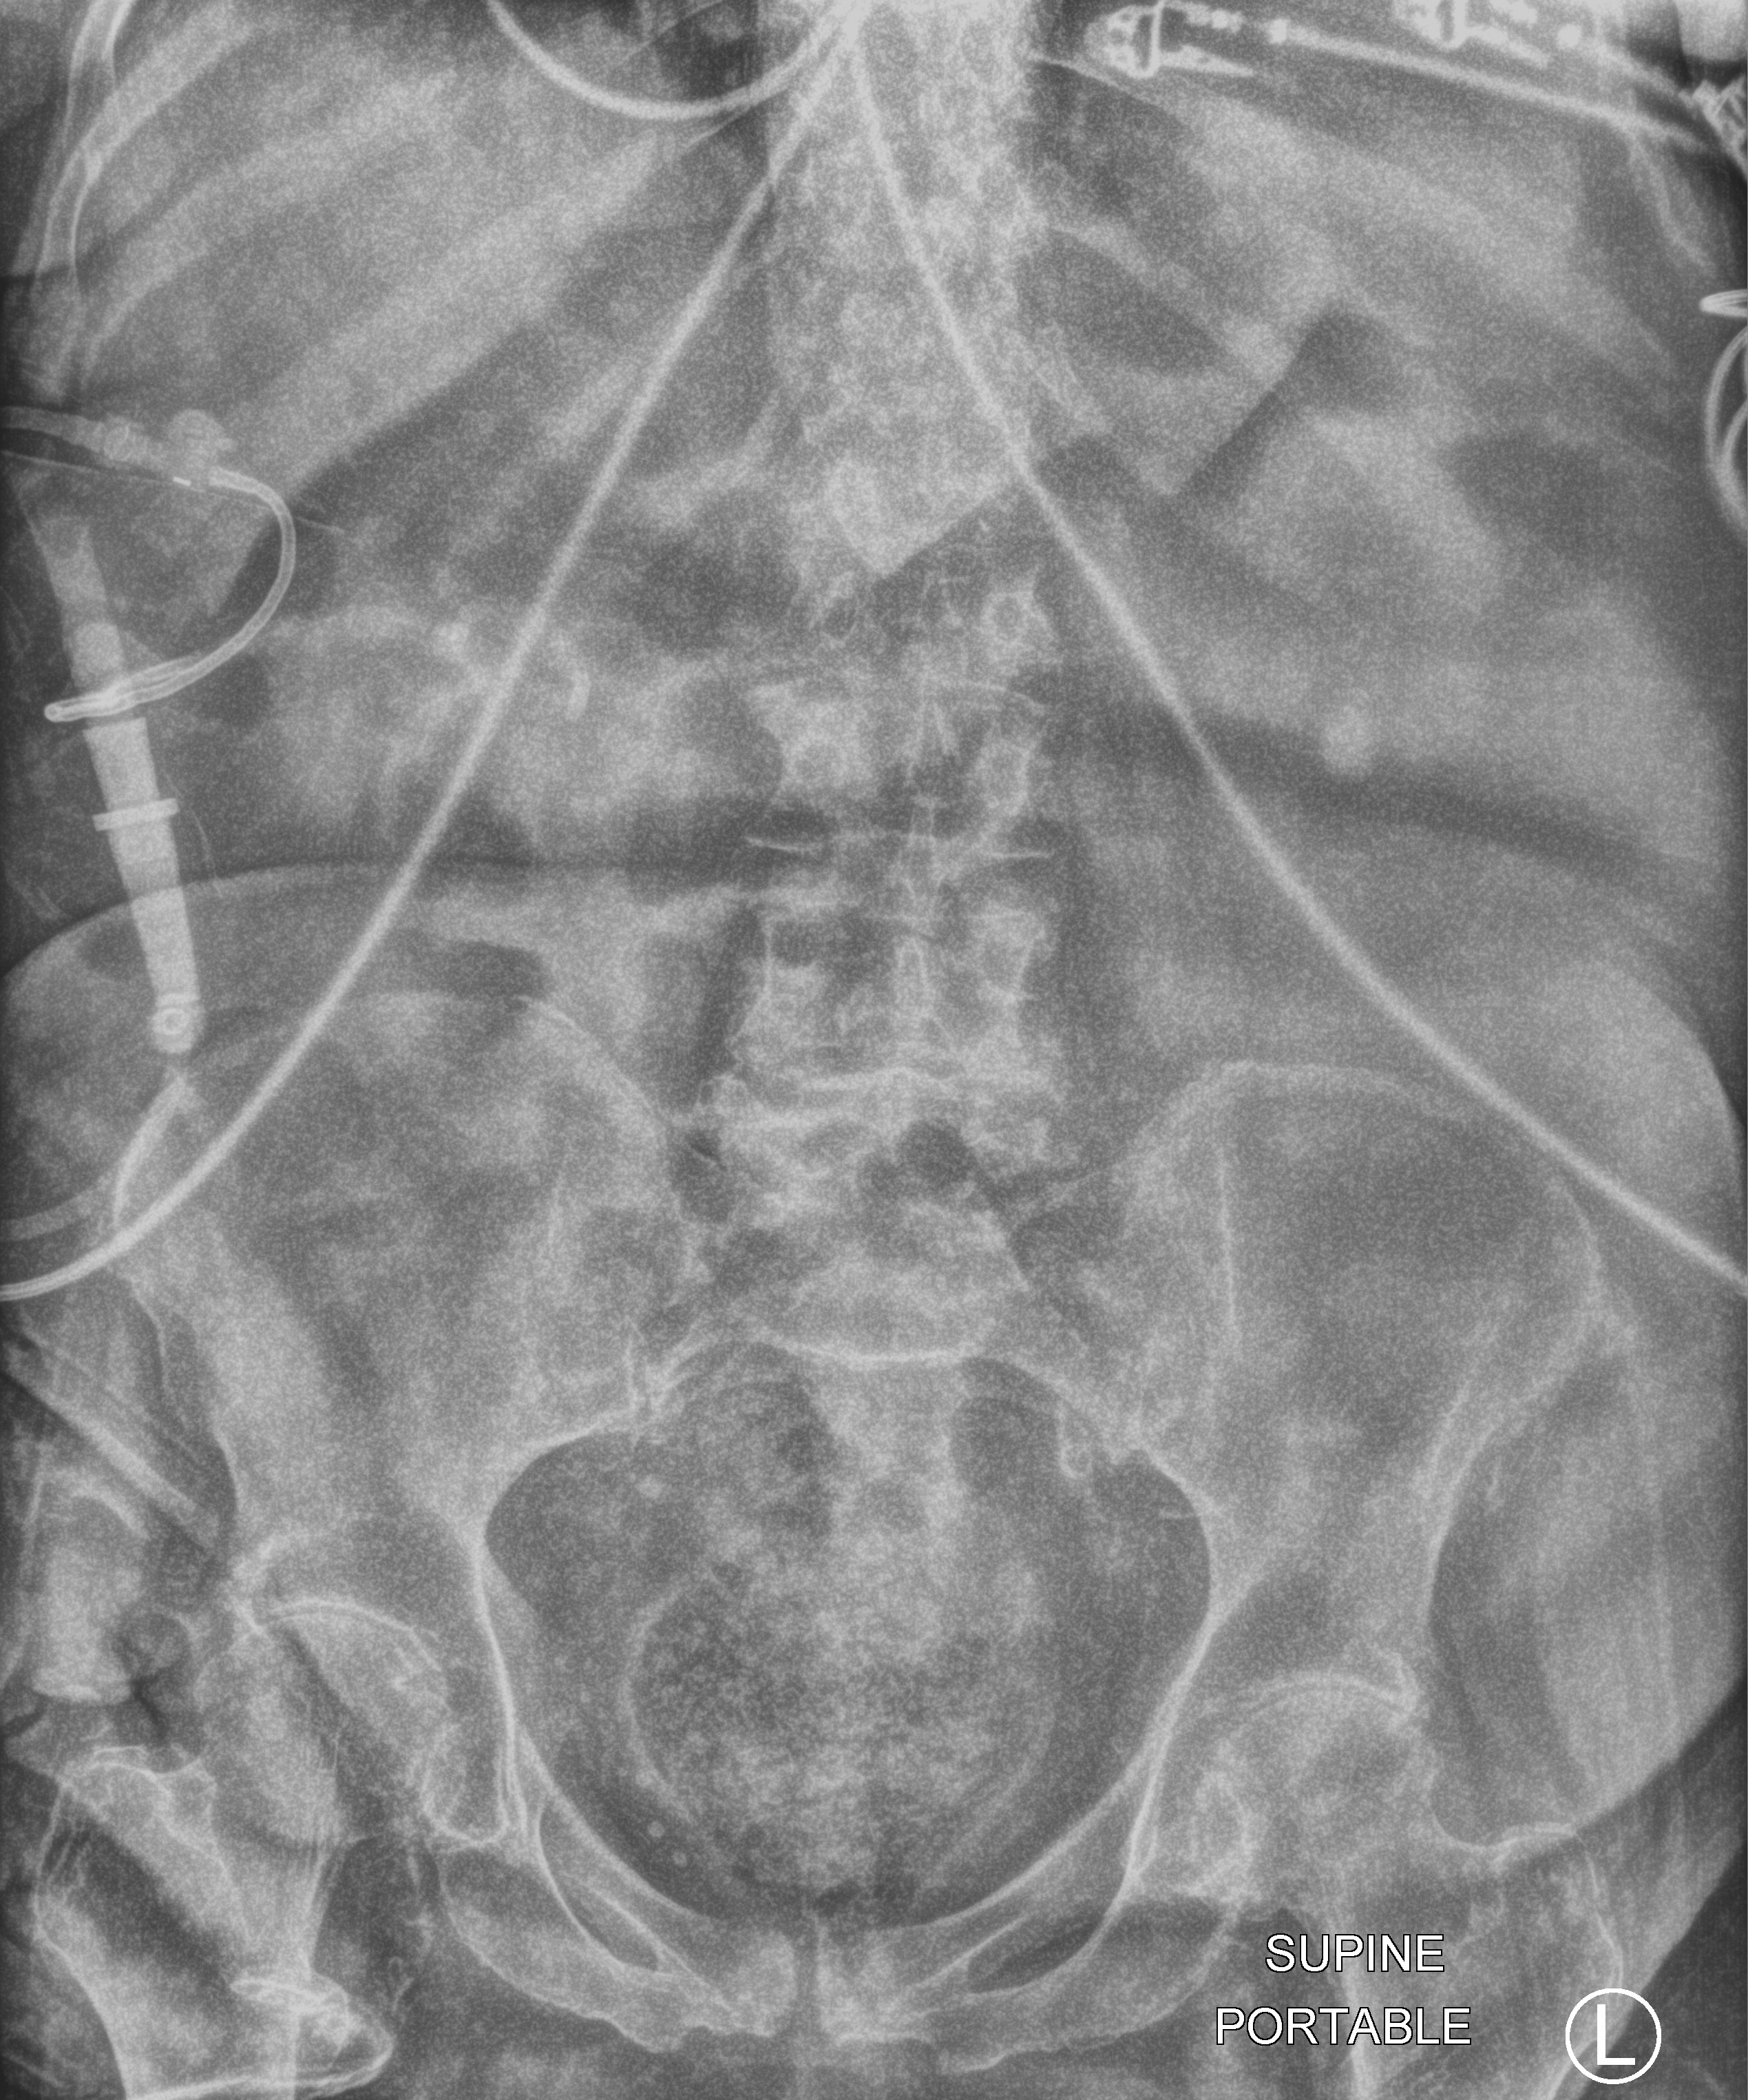
Bedside abdomen radiograph (computed radiography); anteroposterior (AP) projection. Patient hospitalised with COVID-19; female, aged 75–90 years.
Hospital-stay facts (about this admission, not read from this image; timing relative to this image not recorded): hypertension (admission record): yes; mechanically ventilated during this hospital stay: no; COPD (admission record): yes.